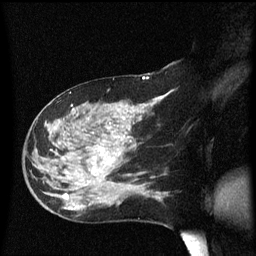
Breast MRI (dynamic contrast-enhanced), one sagittal slice; position 30 of 60 along the scan axis; dynamic contrast-enhanced series, image 2 of 3 at this slice position (ordered by acquisition); 1.5 T; TE 4.2 ms, TR 8.4 ms; 256 × 256 image matrix, field of view 200 × 200 mm. Patient: female, 47 years.
Outlined on this slice (semi-automatic segmentation, software-assisted and operator-edited):
- analysis volume of interest (the breast-tissue region the enhancement analysis was run in; not a lesion): bounding box (x1, y1, x2, y2) in pixels: (24, 97, 149, 206)
- tumour enhancement mask (voxels above the 70 % enhancement threshold inside the analysis volume of interest): (62, 111, 135, 200)